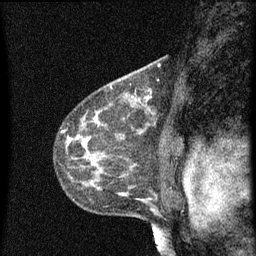
Breast MRI (dynamic contrast-enhanced), one sagittal slice; slice 36 of 60 in the series (ordered by position); dynamic contrast-enhanced series, image 2 of 3 at this slice position (ordered by acquisition); 1.5 T; TE 4.2 ms, TR 8 ms; 2 mm slice thickness; 256 × 256 image matrix, field of view 180 × 180 mm. Female patient, age 41 years.
Outlined on this slice (semi-automatic segmentation, software-assisted and operator-edited):
- analysis volume of interest (the breast-tissue region the enhancement analysis was run in; not a lesion): bounding box <130,76,153,103> (left, top, right, bottom; pixels)
- tumour enhancement mask (voxels above the 70 % enhancement threshold inside the analysis volume of interest): <132,90,151,99>